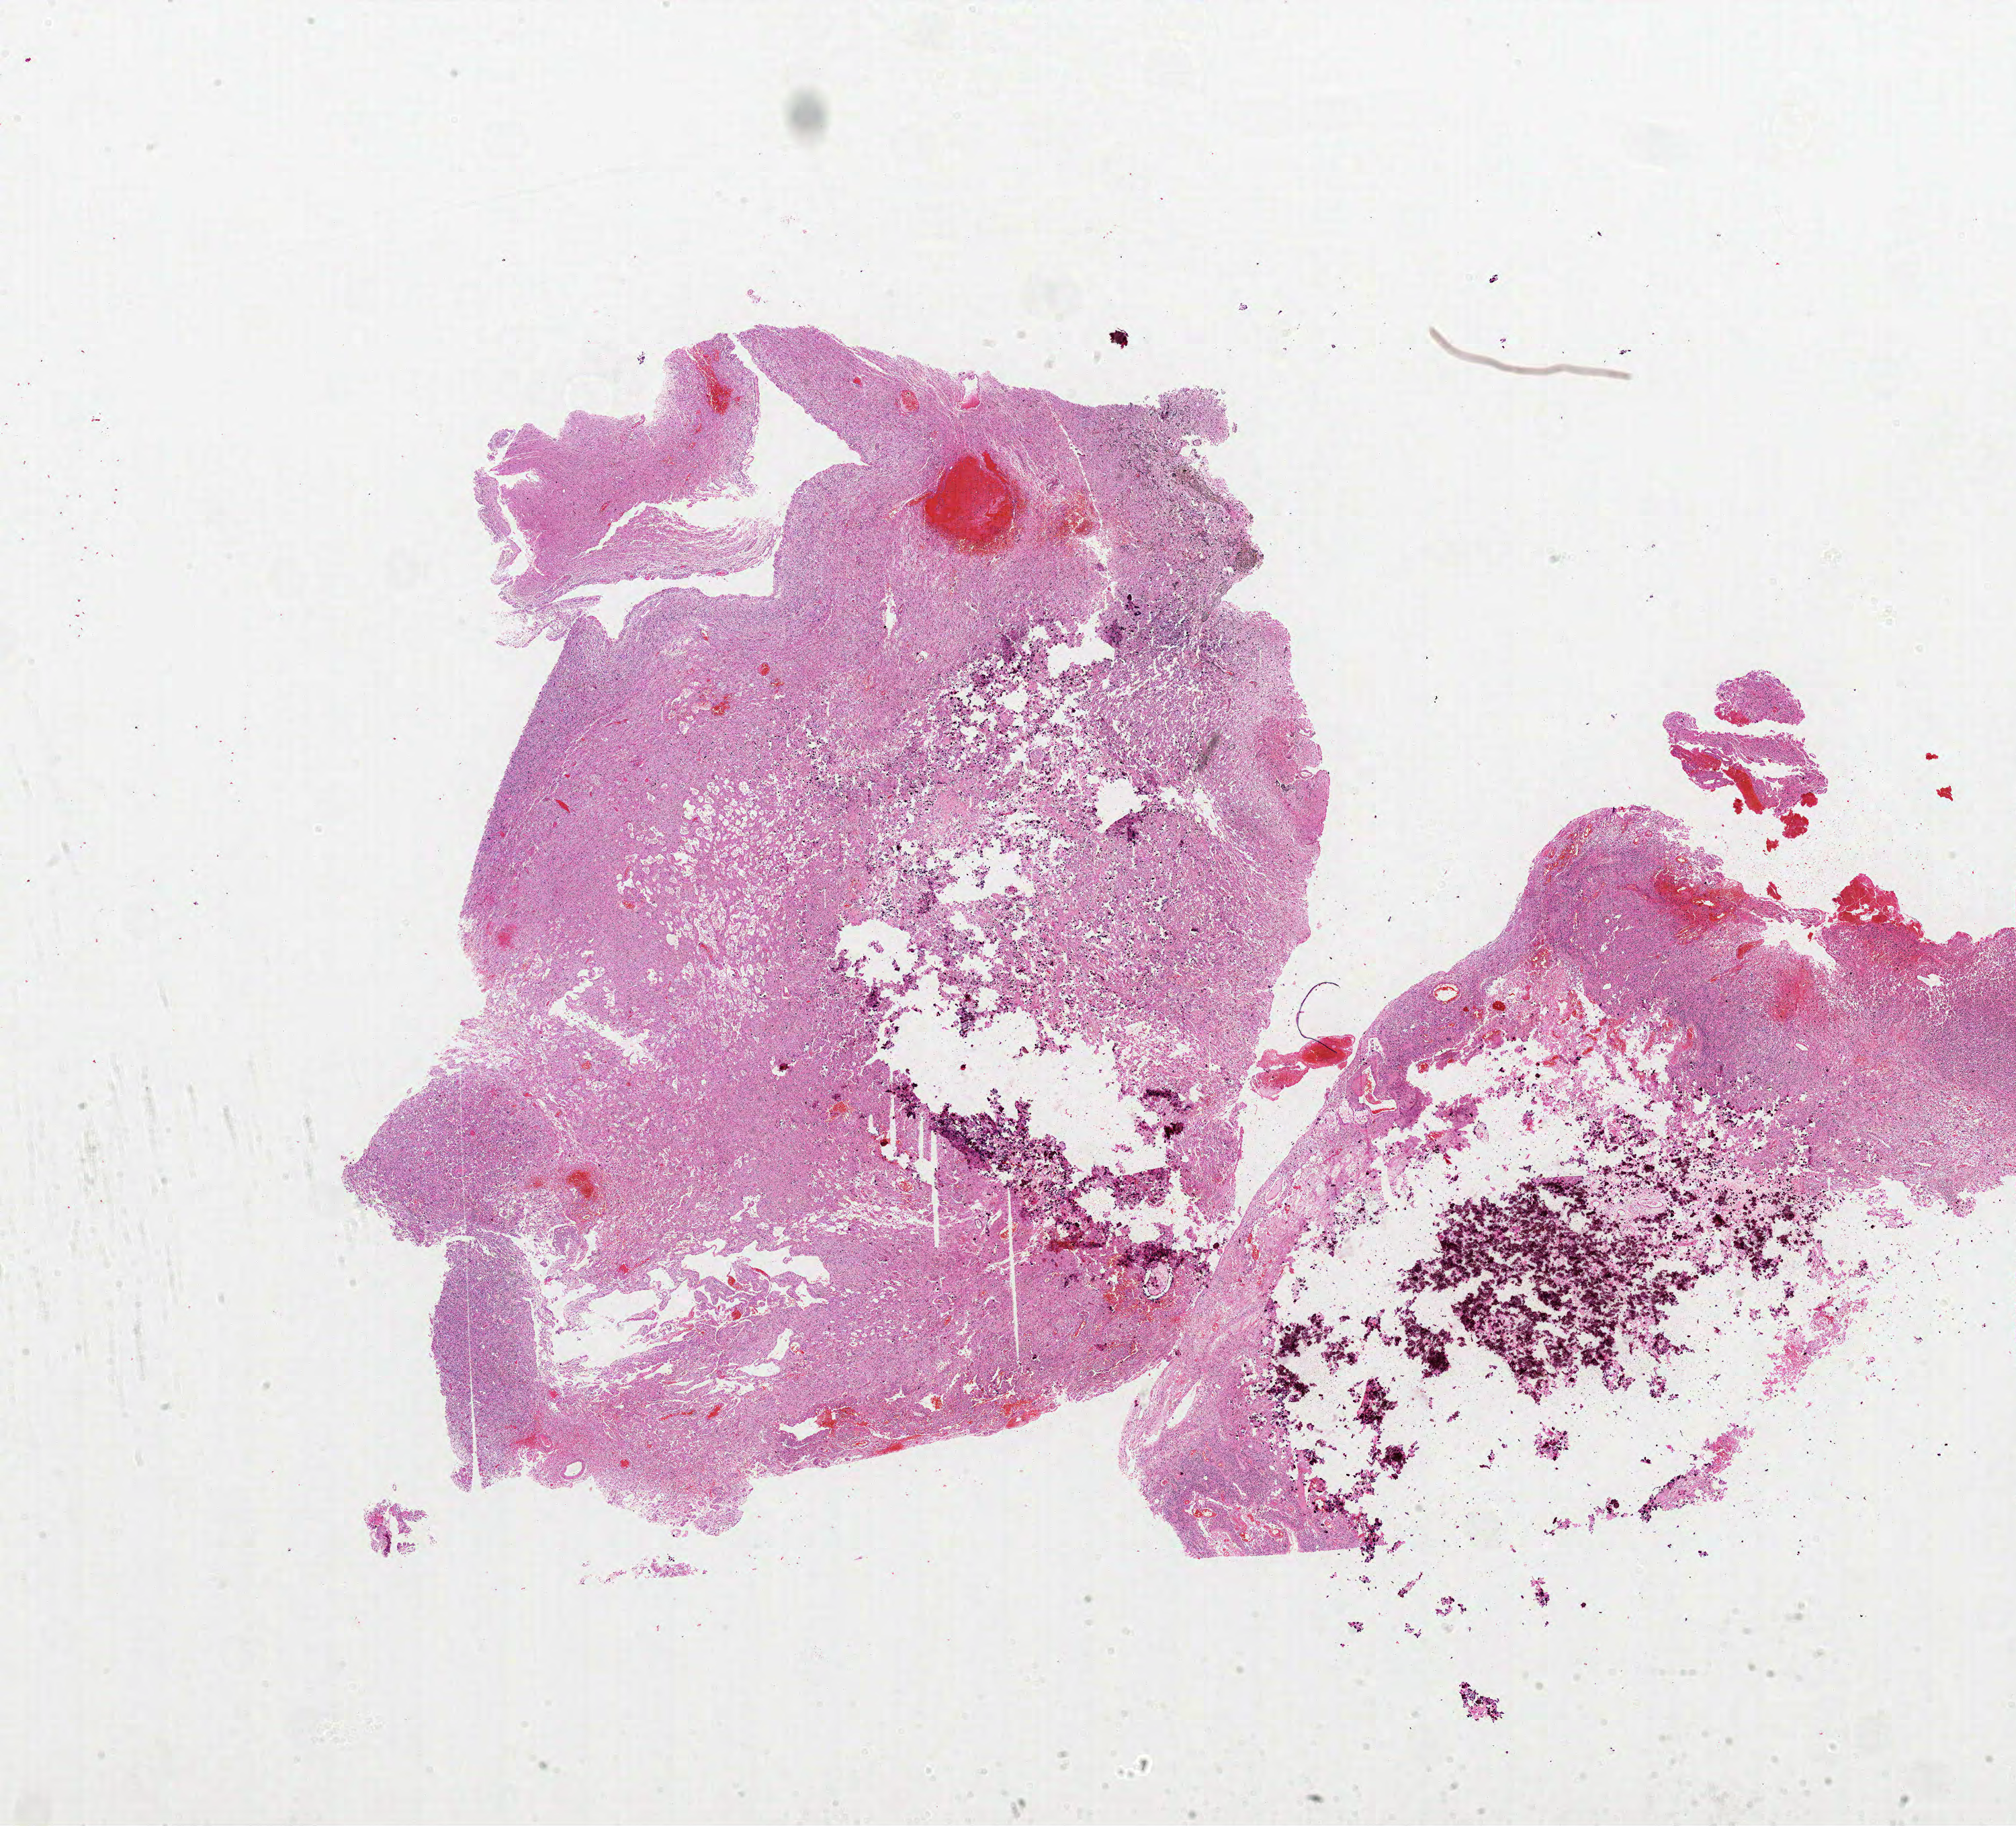
Hematoxylin and eosin (H&E) stained whole-slide image, whole scanned area (about 24.0 x 21.7 mm, slide scanned at 20x) shown as a low-resolution overview, formalin-fixed paraffin-embedded (FFPE) diagnostic section, brain, primary tumour sample. Patient: female, age at initial diagnosis 38 years.
Pathologic diagnosis: Glioblastoma.